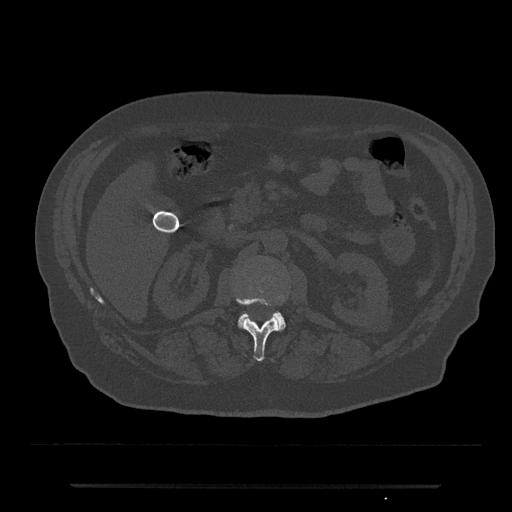
CT including the spine, one axial slice. Position 512 of 797 along the scan axis. 120 kVp. Bone window (W 1800 / L 400 HU). 512 × 512 image matrix. Patient: male, 80 years. From the clinical record (not read from this slice): primary cancer: prostate.
Structures marked on this image (semi-automatic segmentation, software-assisted and operator-edited):
- L1 vertebra: bounding box <236,298,280,361> (left, top, right, bottom; pixels)
- L2 vertebra: <237,312,286,331>